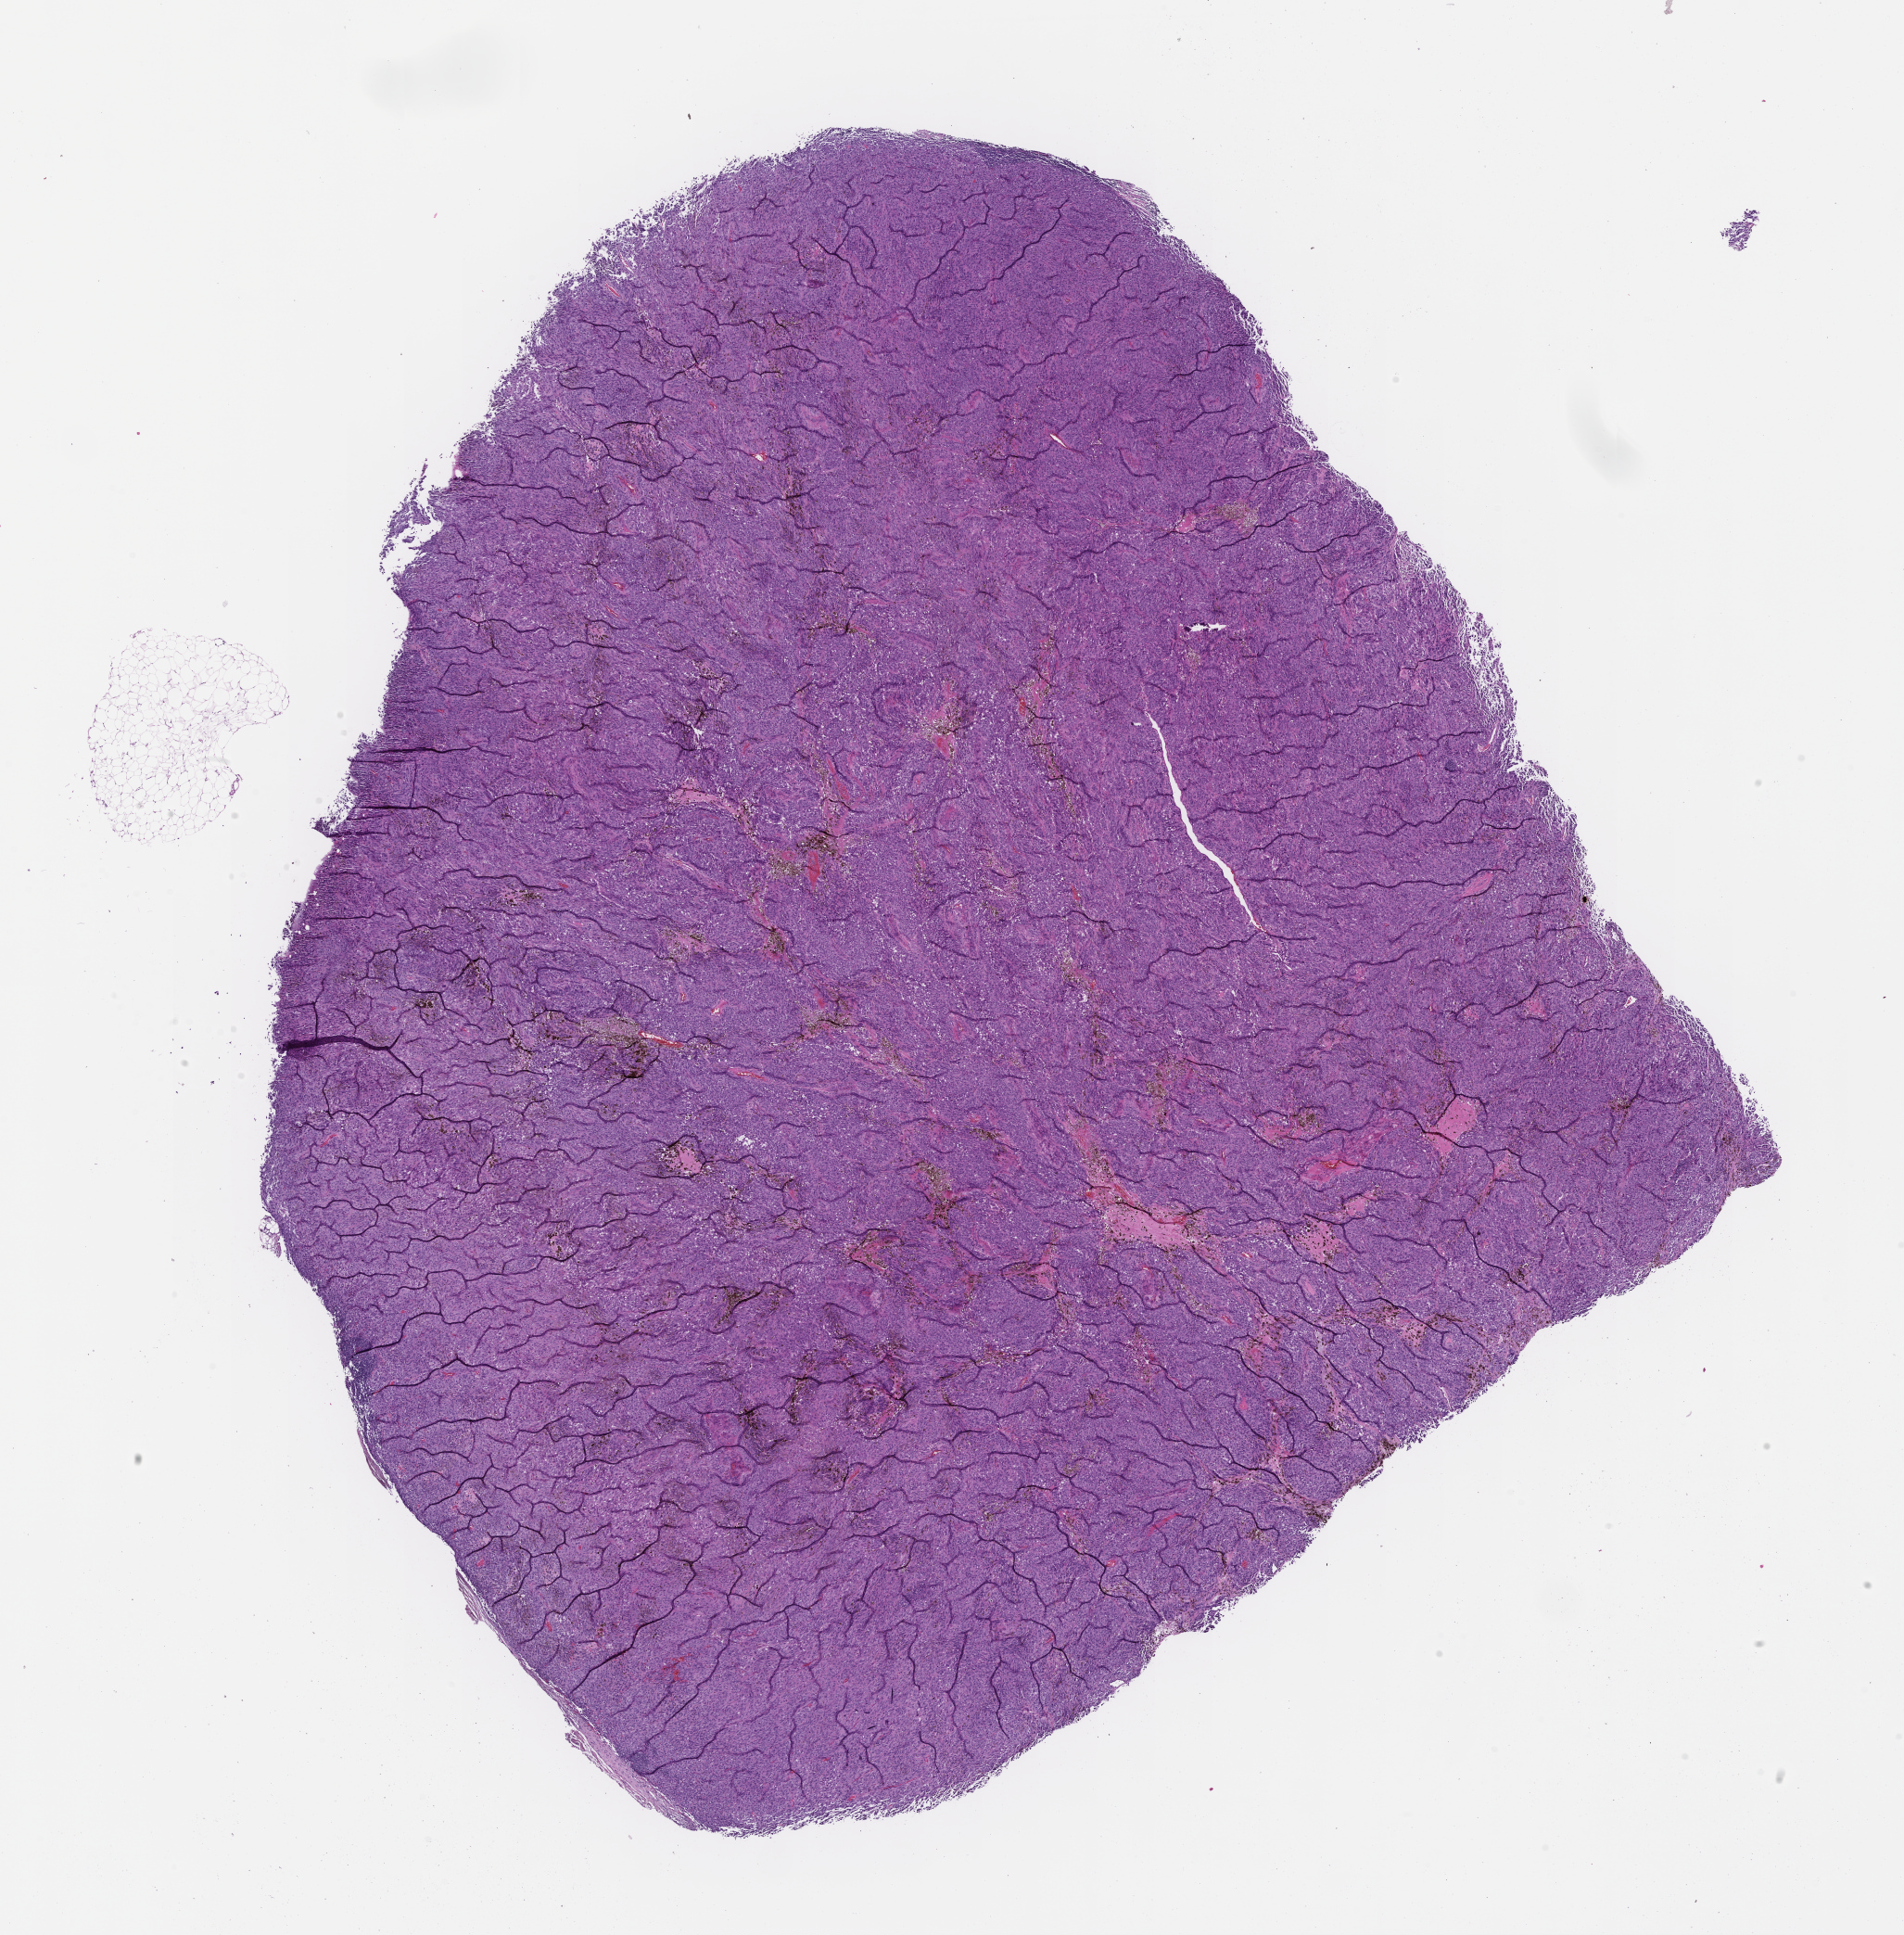
Whole-slide image, hematoxylin and eosin (H&E) stain — whole scanned area (about 16.6 x 16.9 mm) shown as a low-resolution overview; FFPE section; specimen time point: collected at baseline (before treatment). Female patient.
This section: metastatic tumor tissue. Primary diagnosis of the patient: Melanoma.